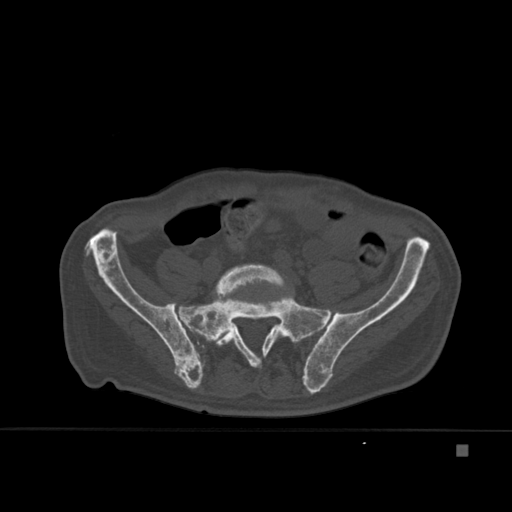
CT including the spine, one axial slice. Position 92 of 451 along the scan axis. Bone window (W 1800 / L 400 HU). 1.5 mm slice thickness. 512 × 512 image matrix, field of view 378 × 378 mm. Male patient, age 75 years. Case-level facts recorded for this patient, not image findings: primary cancer: prostate.
Structures marked on this image (semi-automatic segmentation, software-assisted and operator-edited):
- L5 vertebra: bounding box <213,264,285,353> (left, top, right, bottom; pixels)